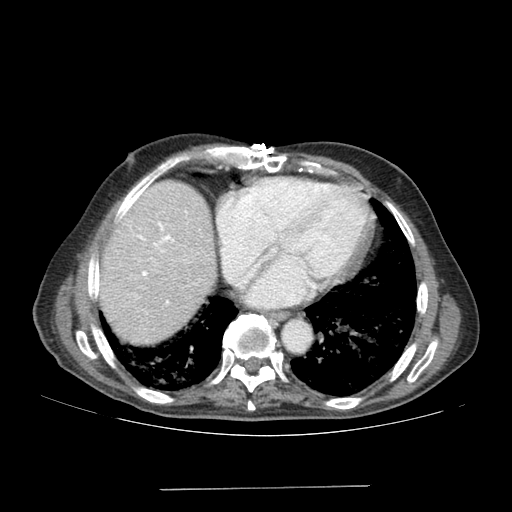
Contrast-enhanced abdominal CT (liver protocol), one axial slice; slice 160 of 192 in the series (ordered by position); reconstruction kernel SOFT; 120 kVp; soft-tissue window (W 400 / L 40 HU); 512 × 512 image matrix, field of view 400 × 400 mm. From the clinical record (not read from this slice): diagnosis: hepatocellular carcinoma (patient treated with transarterial chemoembolisation; whether this scan precedes or follows treatment is not stated here); TNM stage (as recorded): Stage-IVA; Child-Pugh class: A; tumour differentiation: poorly differentiated; tumour nodularity: uninodular.
Annotated regions visible in this slice (semi-automatic segmentation, software-assisted and operator-edited):
- liver parenchyma outside the tumour (the mass and vessels are separate outlines, so this box may not span the whole liver): bounding box <98,180,216,344> (left, top, right, bottom; pixels)
- liver vessels: <122,210,174,303>